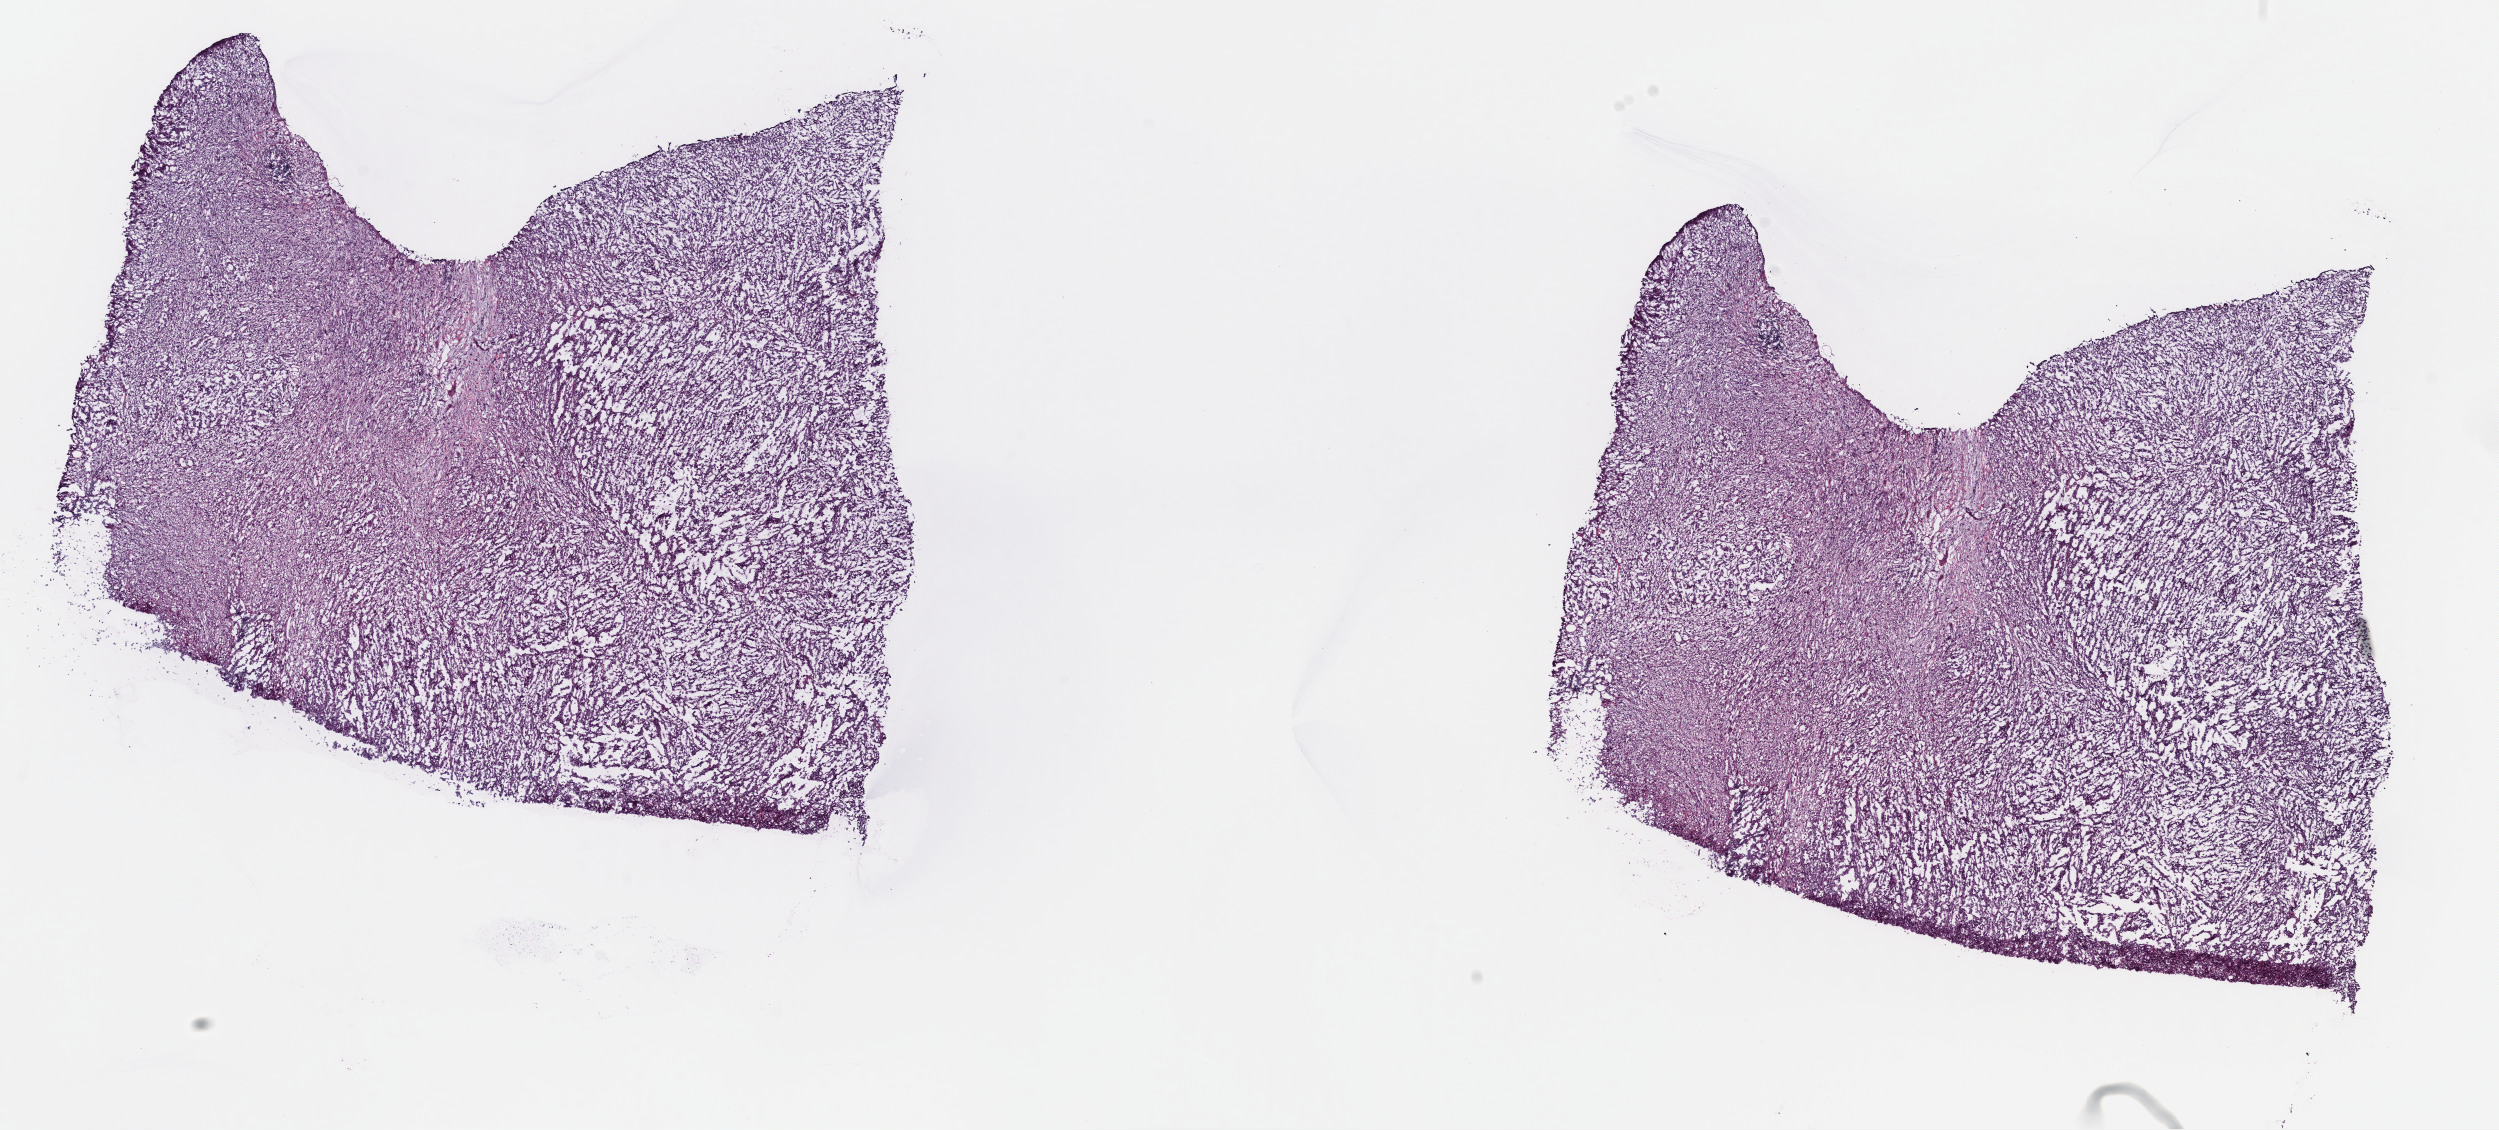
H&E whole-slide image, low-resolution overview of the scanned area, about 19.7 x 8.9 mm (acquisition: 40x scan), frozen section from the top of the tissue portion, metastatic tumour sample. Male, age 33 years at initial diagnosis. Composition of this section per pathologist review: tumour cells 85%, tumour nuclei 85%, normal cells 0%, stromal cells 14%, necrosis 1%. Infiltration values recorded for this section: lymphocyte infiltration 3%, monocyte infiltration 2%, neutrophil infiltration 0%.
This section: metastatic tumour tissue. Patient diagnosis: Malignant melanoma, NOS.